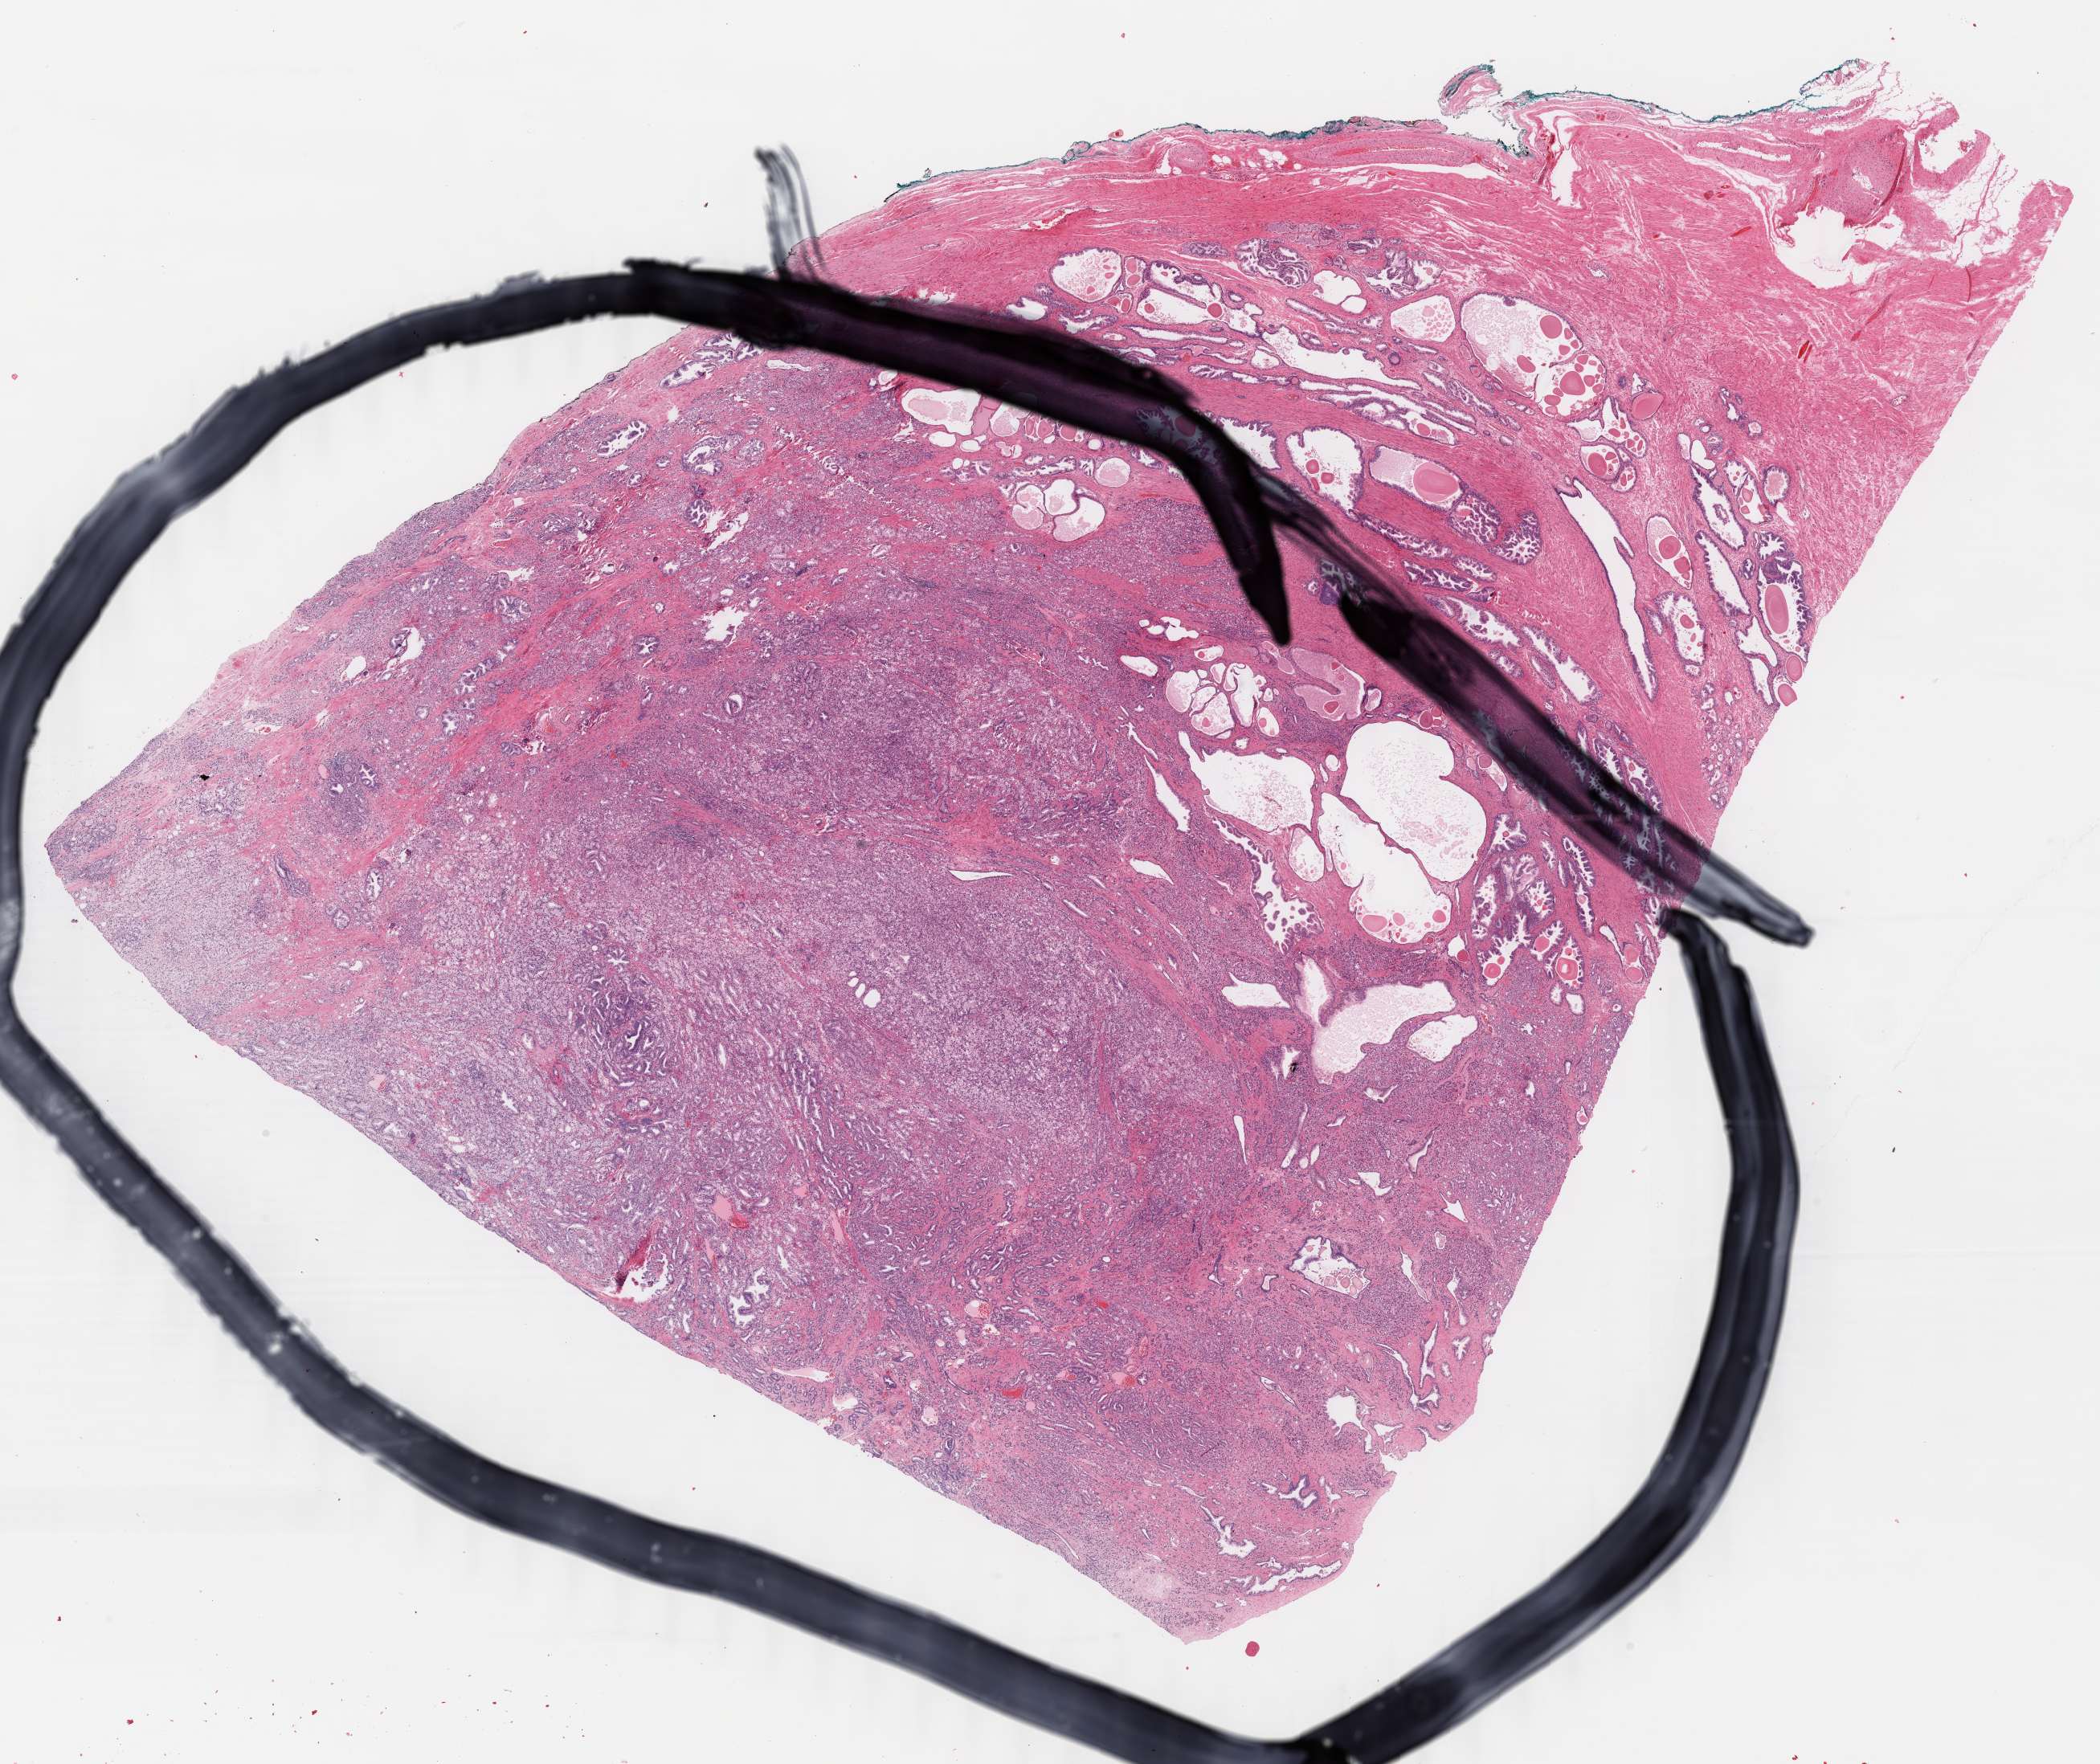
Hematoxylin and eosin (H&E) stained whole-slide image, a low-resolution overview of the entire scanned area, about 20.8 x 17.5 mm (slide scanned at 40x). Formalin-fixed paraffin-embedded (FFPE) diagnostic section. Prostate, primary tumour sample. Male, age 63 years at initial diagnosis. Gleason score: 9 (4+5).
• diagnosis: Adenocarcinoma, NOS (prostate gland)
• laterality: bilateral
• lymph nodes positive (case pathology): 0 of 5 examined